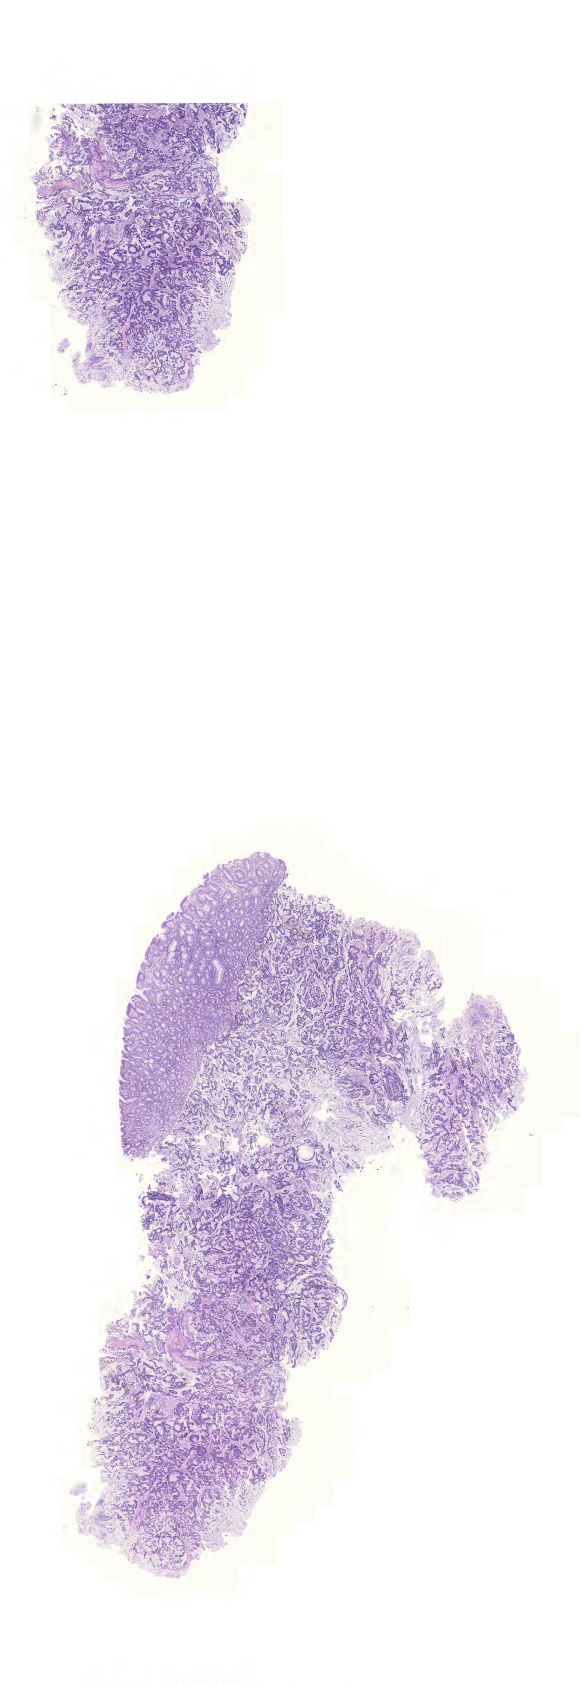
Whole-slide histology image, H&E-stained — whole scanned area (about 8.6 x 25.1 mm, slide scanned at 20x) shown as a low-resolution overview; formalin-fixed paraffin-embedded (FFPE) diagnostic section; rectum, primary tumour sample. Patient: female, age at initial diagnosis 83 years.
* AJCC pathologic stage: IIA
* lymph nodes positive (case pathology): 0 of 30 examined
* diagnosis: Mucinous adenocarcinoma (unknown primary site)